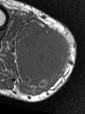
MRI of an extremity soft-tissue mass, one axial slice. Slice 28 of 47 in the series (ordered by position). MR volume resampled by the dataset authors to the PET/CT grid (not the native acquisition matrix). 3.27 mm slice thickness. 85 × 114 image matrix. Male patient. From the clinical record (not read from this slice): histological type: pleiomorphic liposarcoma; grade: high; site of the primary tumour: right calf.
Outlined on this slice (expert contour drawn on MRI and transferred to this co-registered scan by the dataset authors):
- gross tumour volume including surrounding oedema: bounding box [x1, y1, x2, y2] px = [17, 23, 69, 83]
- gross tumour volume (mass): [17, 28, 71, 81]